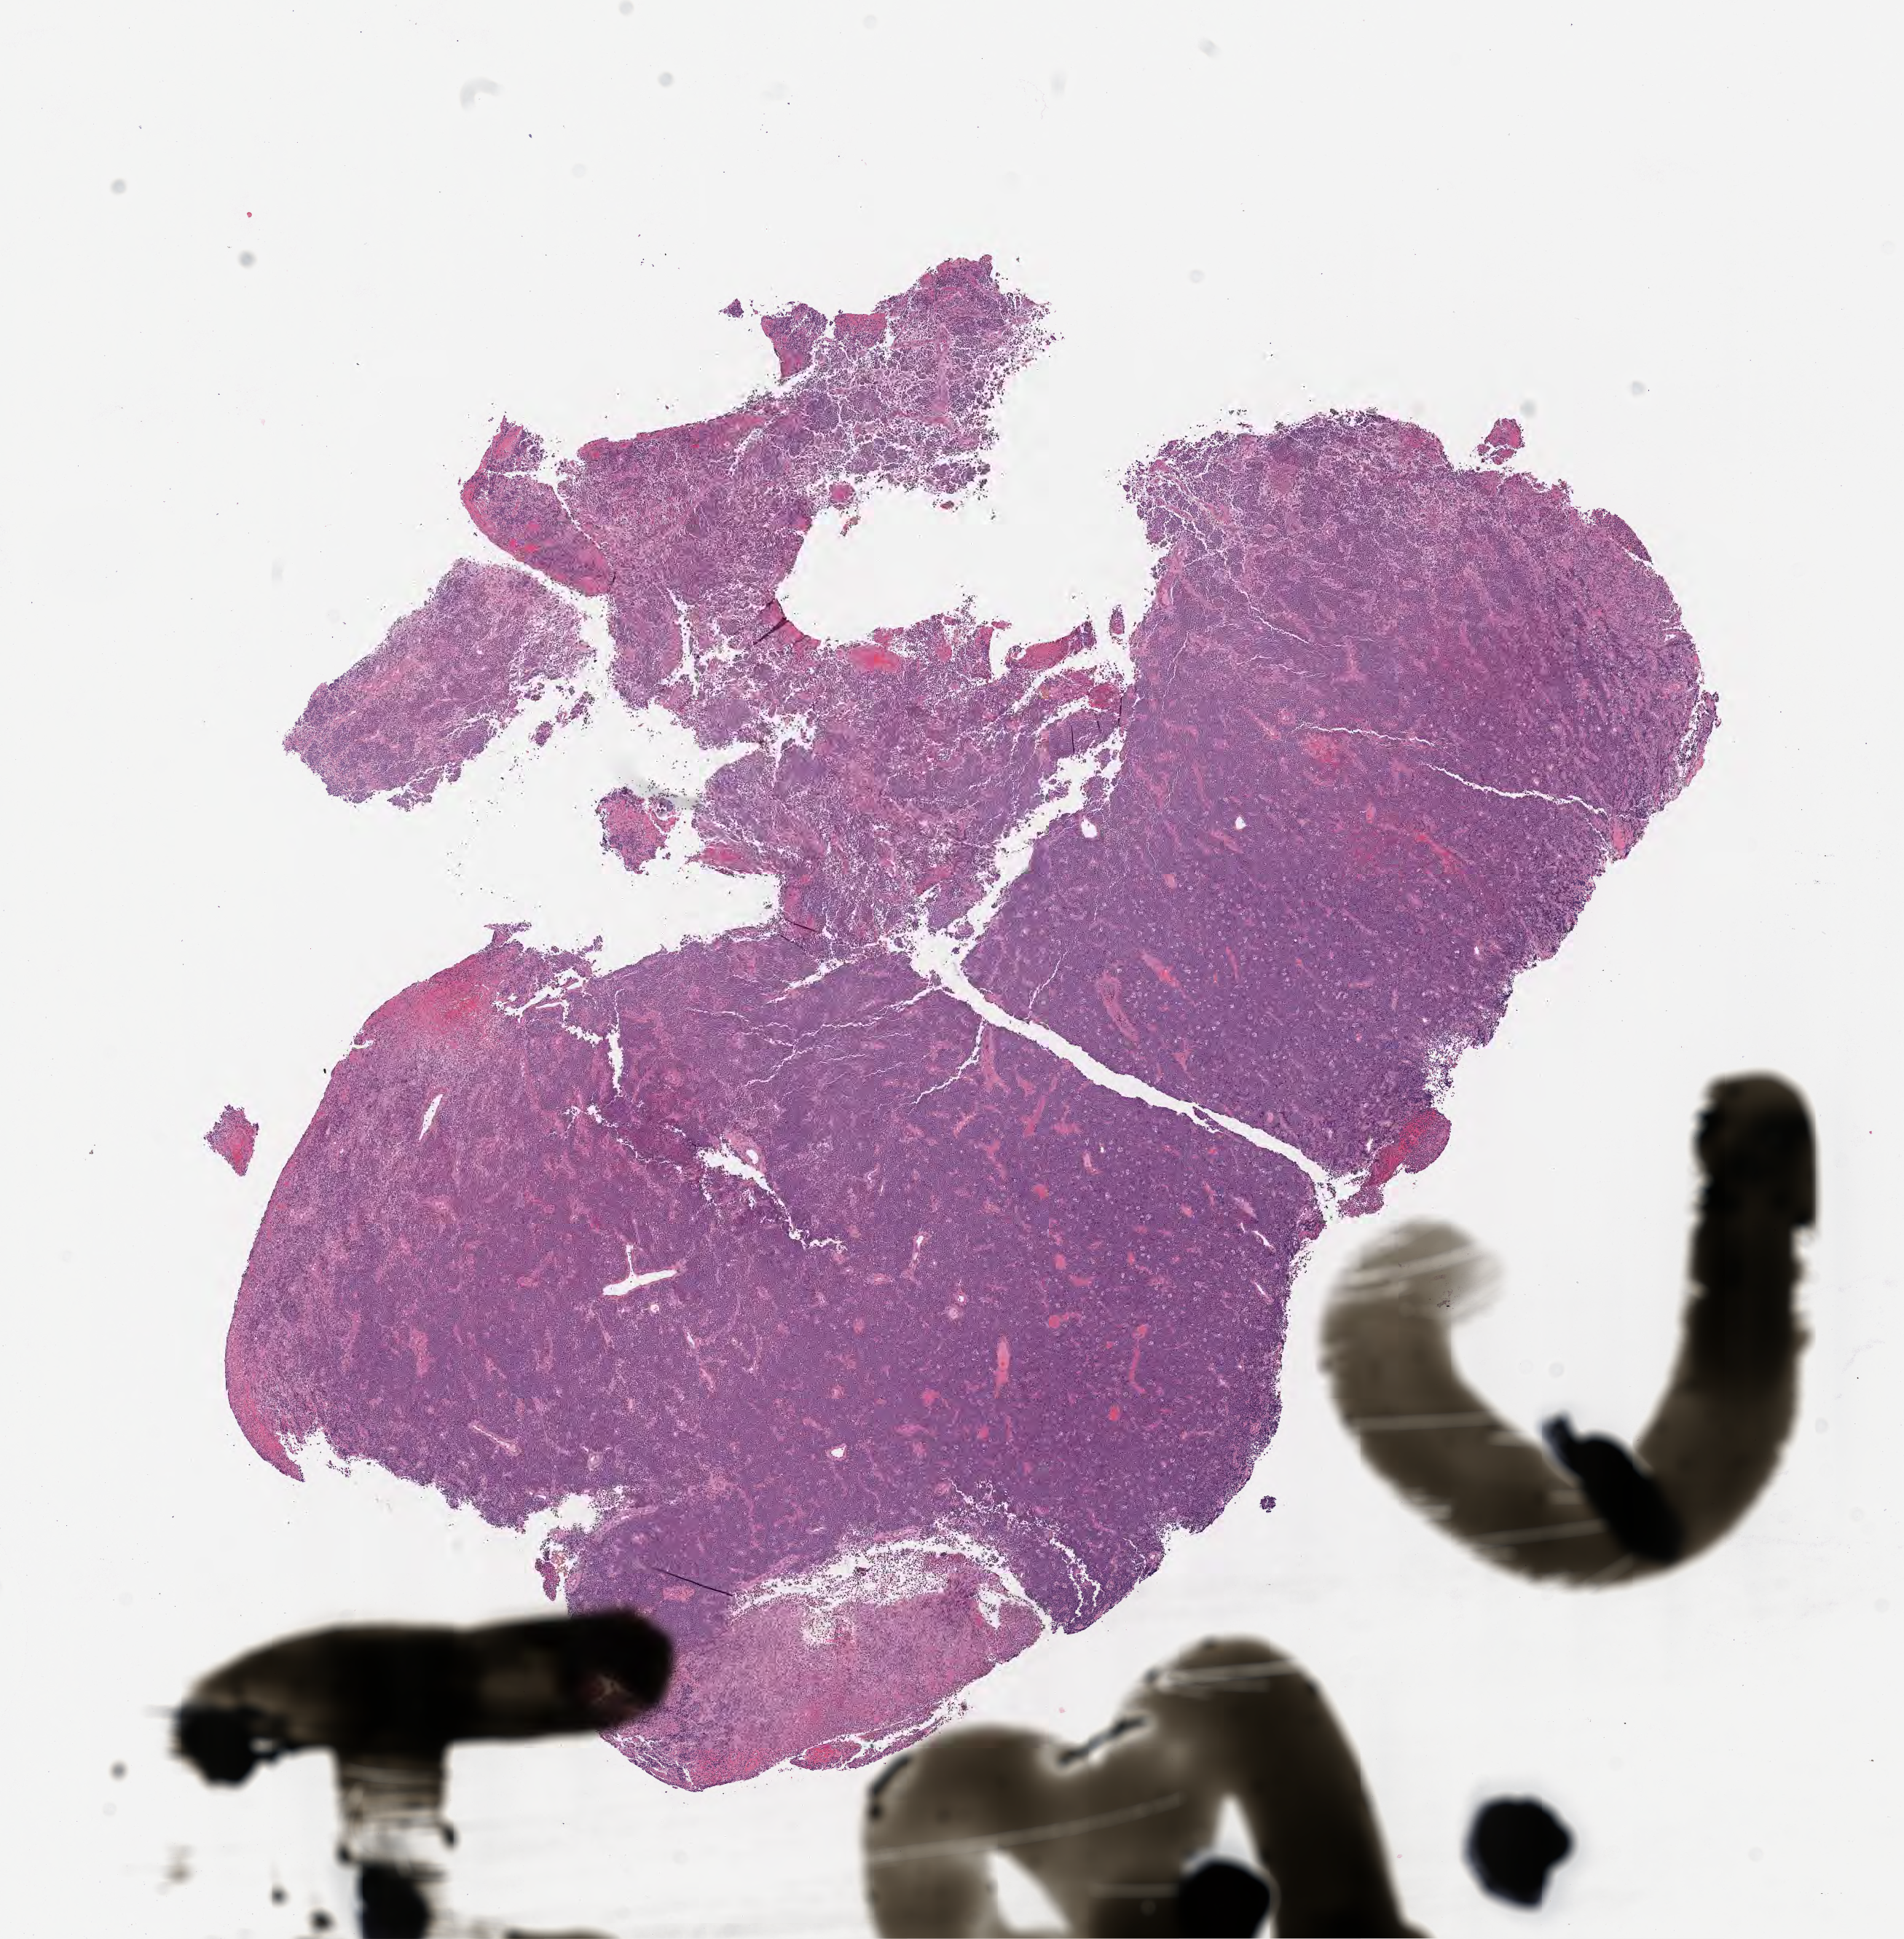
H&E whole-slide image — whole scanned area (about 10.6 x 10.8 mm) shown as a low-resolution overview. Specimen: tumor tissue. Site: cranium. Female patient; age at initial diagnosis 7 years.
* diagnosis: Burkitt lymphoma, NOS